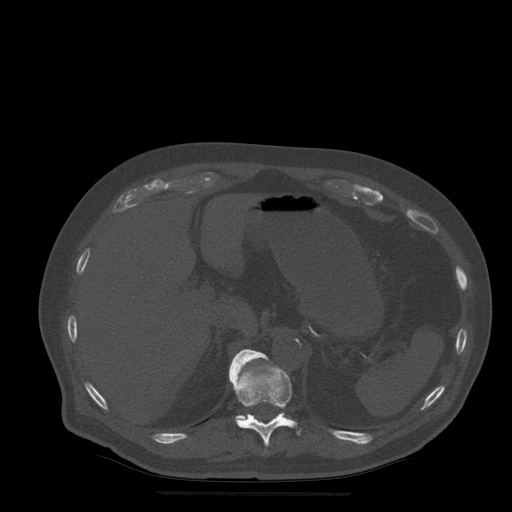
CT including the spine, one axial slice. Position 240 of 522 along the scan axis. Bone window (W 1800 / L 400 HU). 1.25 mm slice thickness. 512 × 512 image matrix, field of view 420 × 420 mm. Patient age 72 years. From the clinical record (not read from this slice): primary cancer: prostate.
Structures marked on this image (semi-automatically segmented with operator editing):
- T11 vertebra: box from (x=229, y=350) to (x=302, y=447) px
- T12 vertebra: (x=229, y=350)–(x=262, y=419)